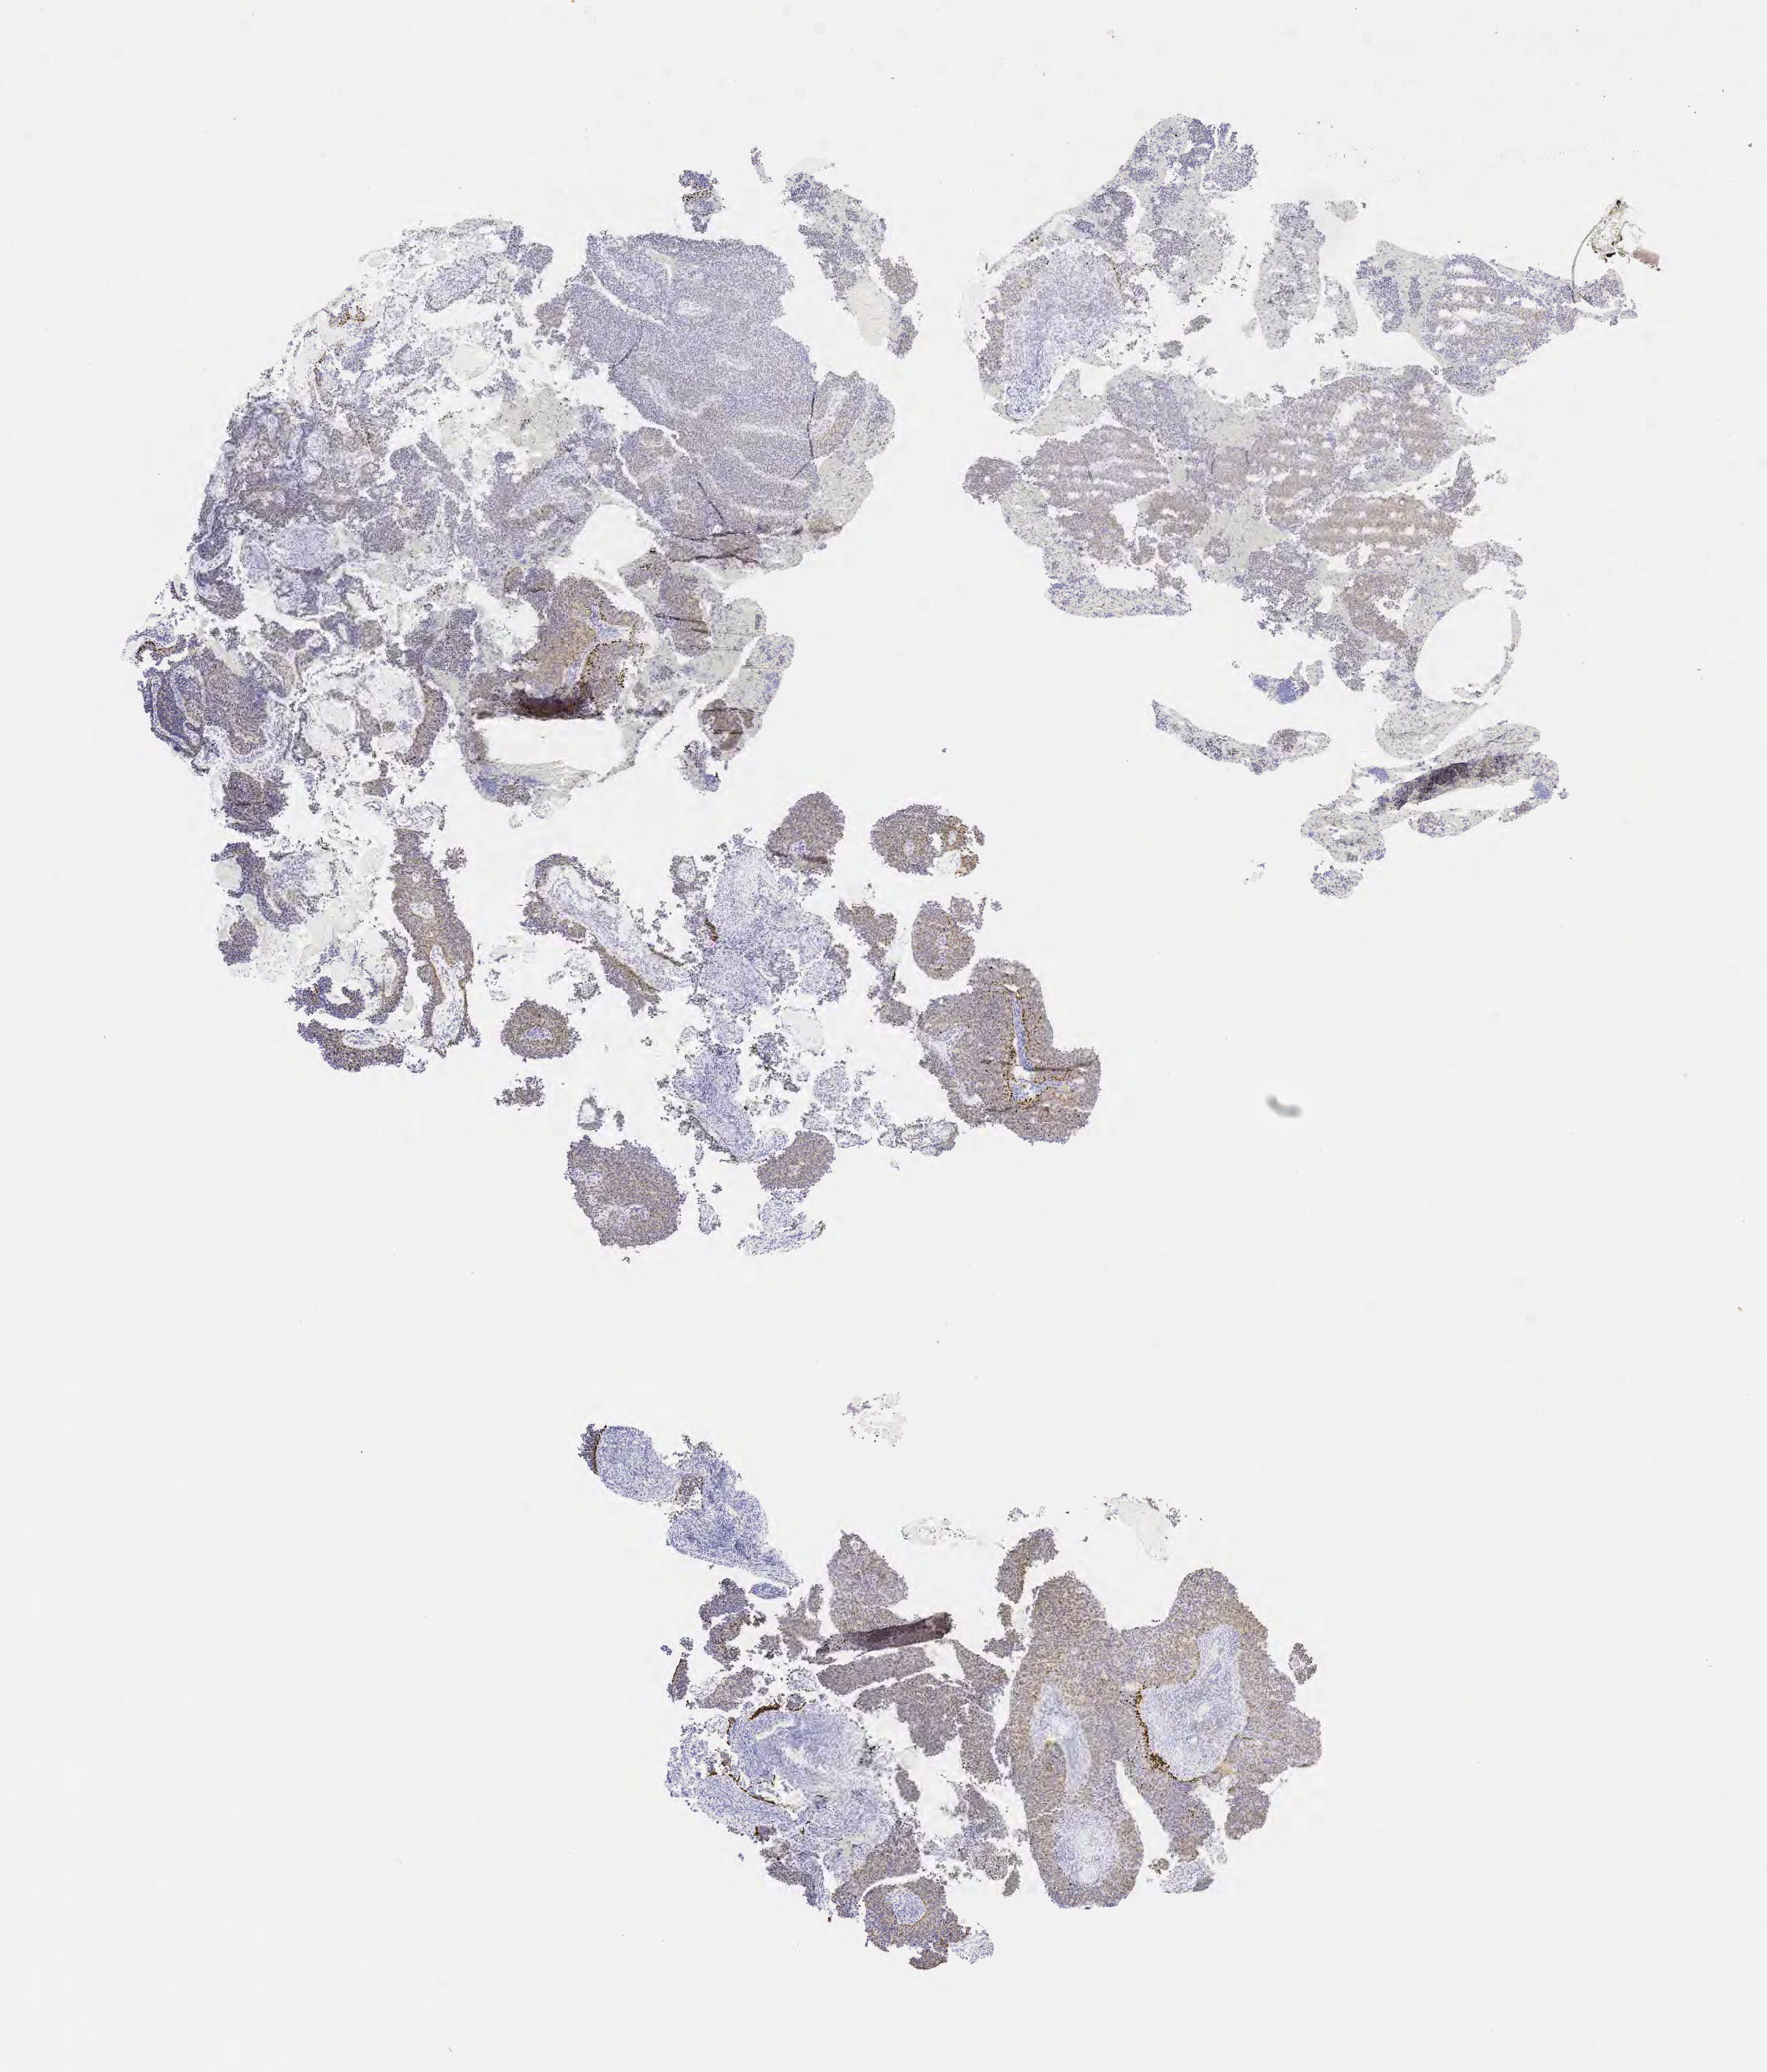
Immunohistochemistry (IHC) whole-slide image stained for p63, whole scanned area (about 9.1 x 10.6 mm) shown as a low-resolution overview. Tumor tissue. Anatomic site: cervix. Patient female; age 44 years.
Diagnosis: Squamous cell carcinoma, large cell, nonkeratinizing, NOS.